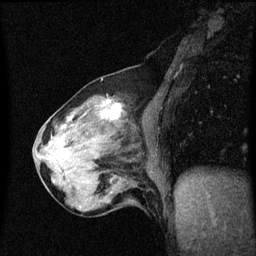
Breast MRI (dynamic contrast-enhanced), one sagittal slice; slice 23 of 60 in the series (ordered by position); dynamic contrast-enhanced series, image 2 of 3 at this slice position (ordered by acquisition); 1.5 T; TE 4.2 ms, TR 8.4 ms; 2 mm slice thickness; 256 × 256 image matrix, field of view 200 × 200 mm. Female patient, age 64 years. From the clinical record (not read from this slice): setting: breast cancer imaged before/during neoadjuvant chemotherapy; receptor status: HR-positive, HER2-negative.
Structures marked on this image (semi-automatically segmented with operator editing):
- analysis volume of interest (the breast-tissue region the enhancement analysis was run in; not a lesion): bounding box <56,98,136,175> (left, top, right, bottom; pixels)
- tumour enhancement mask (voxels above the 70 % enhancement threshold inside the analysis volume of interest): <104,100,122,119>